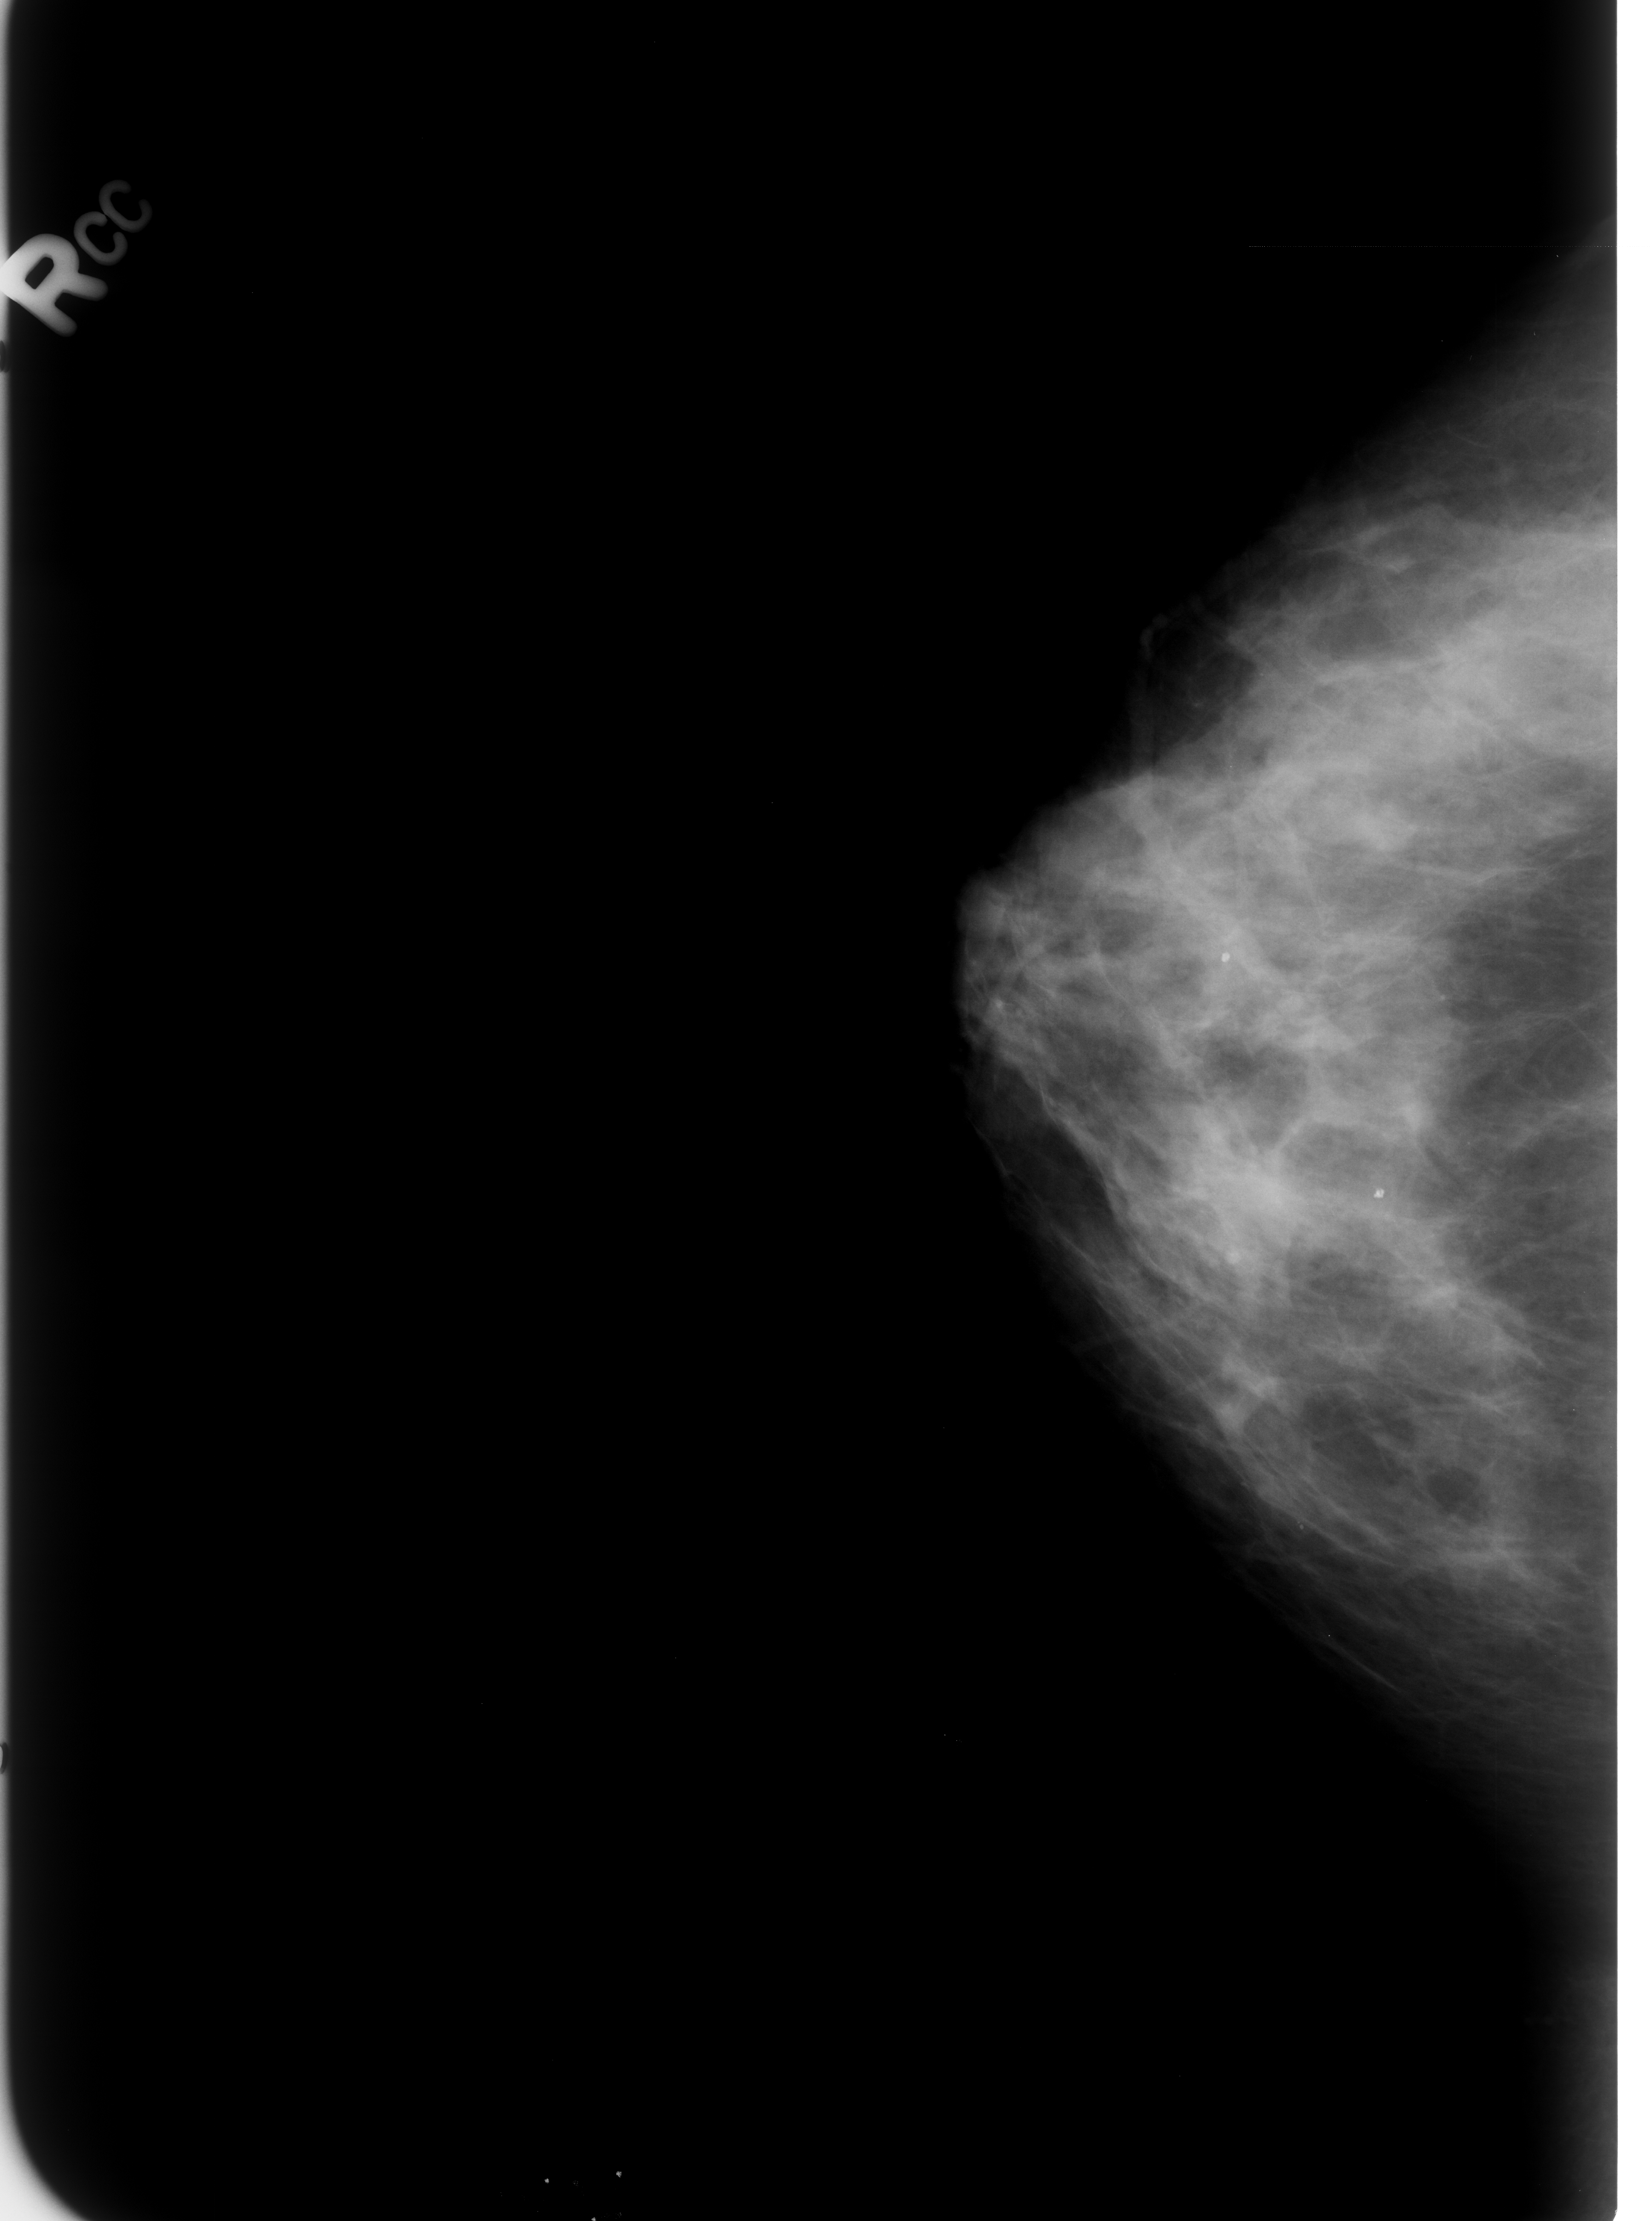
Mammogram (digitized film). Right breast. Craniocaudal (CC) view. BI-RADS breast density category 3 (scale 1–4). 1652 × 2221 image matrix.
Marked abnormalities (boxes around the expert regions of interest):
- Finding 1 of 2: calcifications, morphology lucent center; BI-RADS assessment category 2; benign; no additional work-up was recommended (outcome (as recorded, no biopsy): benign without callback): bounding box (x1, y1, x2, y2) in pixels: (1198, 938, 1258, 1001)
- Finding 2 of 2: calcifications, morphology lucent center; BI-RADS assessment category 2; subtlety rating 5 on a 1 (subtle) to 5 (obvious) scale; outcome (as recorded, no biopsy): benign without callback (not worked up further): (1353, 1176, 1409, 1226)